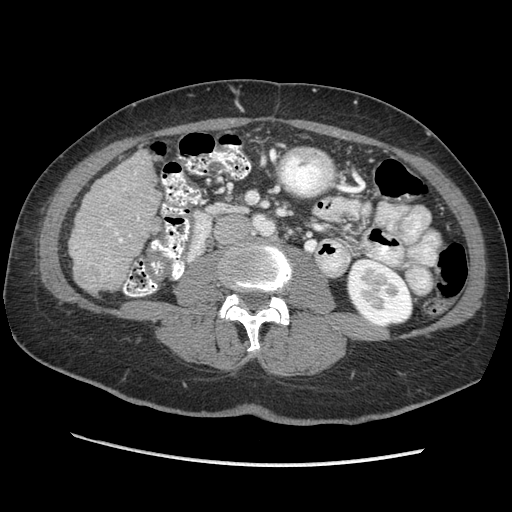
Contrast-enhanced abdominal CT (liver protocol), one axial slice. Position 94 of 170 along the scan axis. 140 kVp. Soft-tissue window (W 400 / L 40 HU). 2.5 mm slice thickness. 512 × 512 image matrix. Case-level facts recorded for this patient, not image findings: diagnosis: hepatocellular carcinoma (patient treated with transarterial chemoembolisation; whether this scan precedes or follows treatment is not stated here); TNM stage (as recorded): Stage-II; Child-Pugh class: A; tumour nodularity: multinodular; tumour size: 4 cm.
Annotated regions visible in this slice (semi-automatic segmentation, software-assisted and operator-edited):
- liver parenchyma outside the tumour (the mass and vessels are separate outlines, so this box may not span the whole liver): bounding box [x1, y1, x2, y2] px = [68, 150, 158, 292]
- liver vessels: [116, 217, 140, 243]